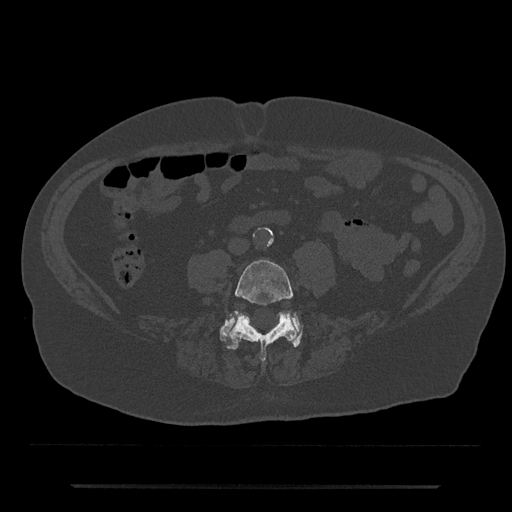
CT including the spine, one axial slice; slice 339 of 797 in the series (ordered by position); 120 kVp; bone window (W 1800 / L 400 HU); 512 × 512 image matrix, field of view 434 × 434 mm. Male patient, age 80 years. Case-level facts recorded for this patient, not image findings: primary cancer: prostate.
Annotated regions visible in this slice (semi-automatically segmented with operator editing):
- L4 vertebra: bounding box (x1, y1, x2, y2) in pixels: (228, 259, 298, 361)
- L5 vertebra: (219, 314, 303, 347)